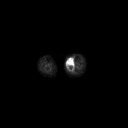
FDG PET of an extremity soft-tissue mass (from a PET/CT study), one axial slice. Position 134 of 223 along the scan axis. 128 × 128 image matrix. Patient: female, 70 years. From the clinical record (not read from this slice): histological type: extraskeletal high grade osteogenic sarcoma; grade: high; site of the primary tumour: left calf.
Annotated regions visible in this slice (expert contour drawn on MRI and transferred to this co-registered scan by the dataset authors):
- gross tumour volume (mass): box from (x=67, y=59) to (x=74, y=69) px